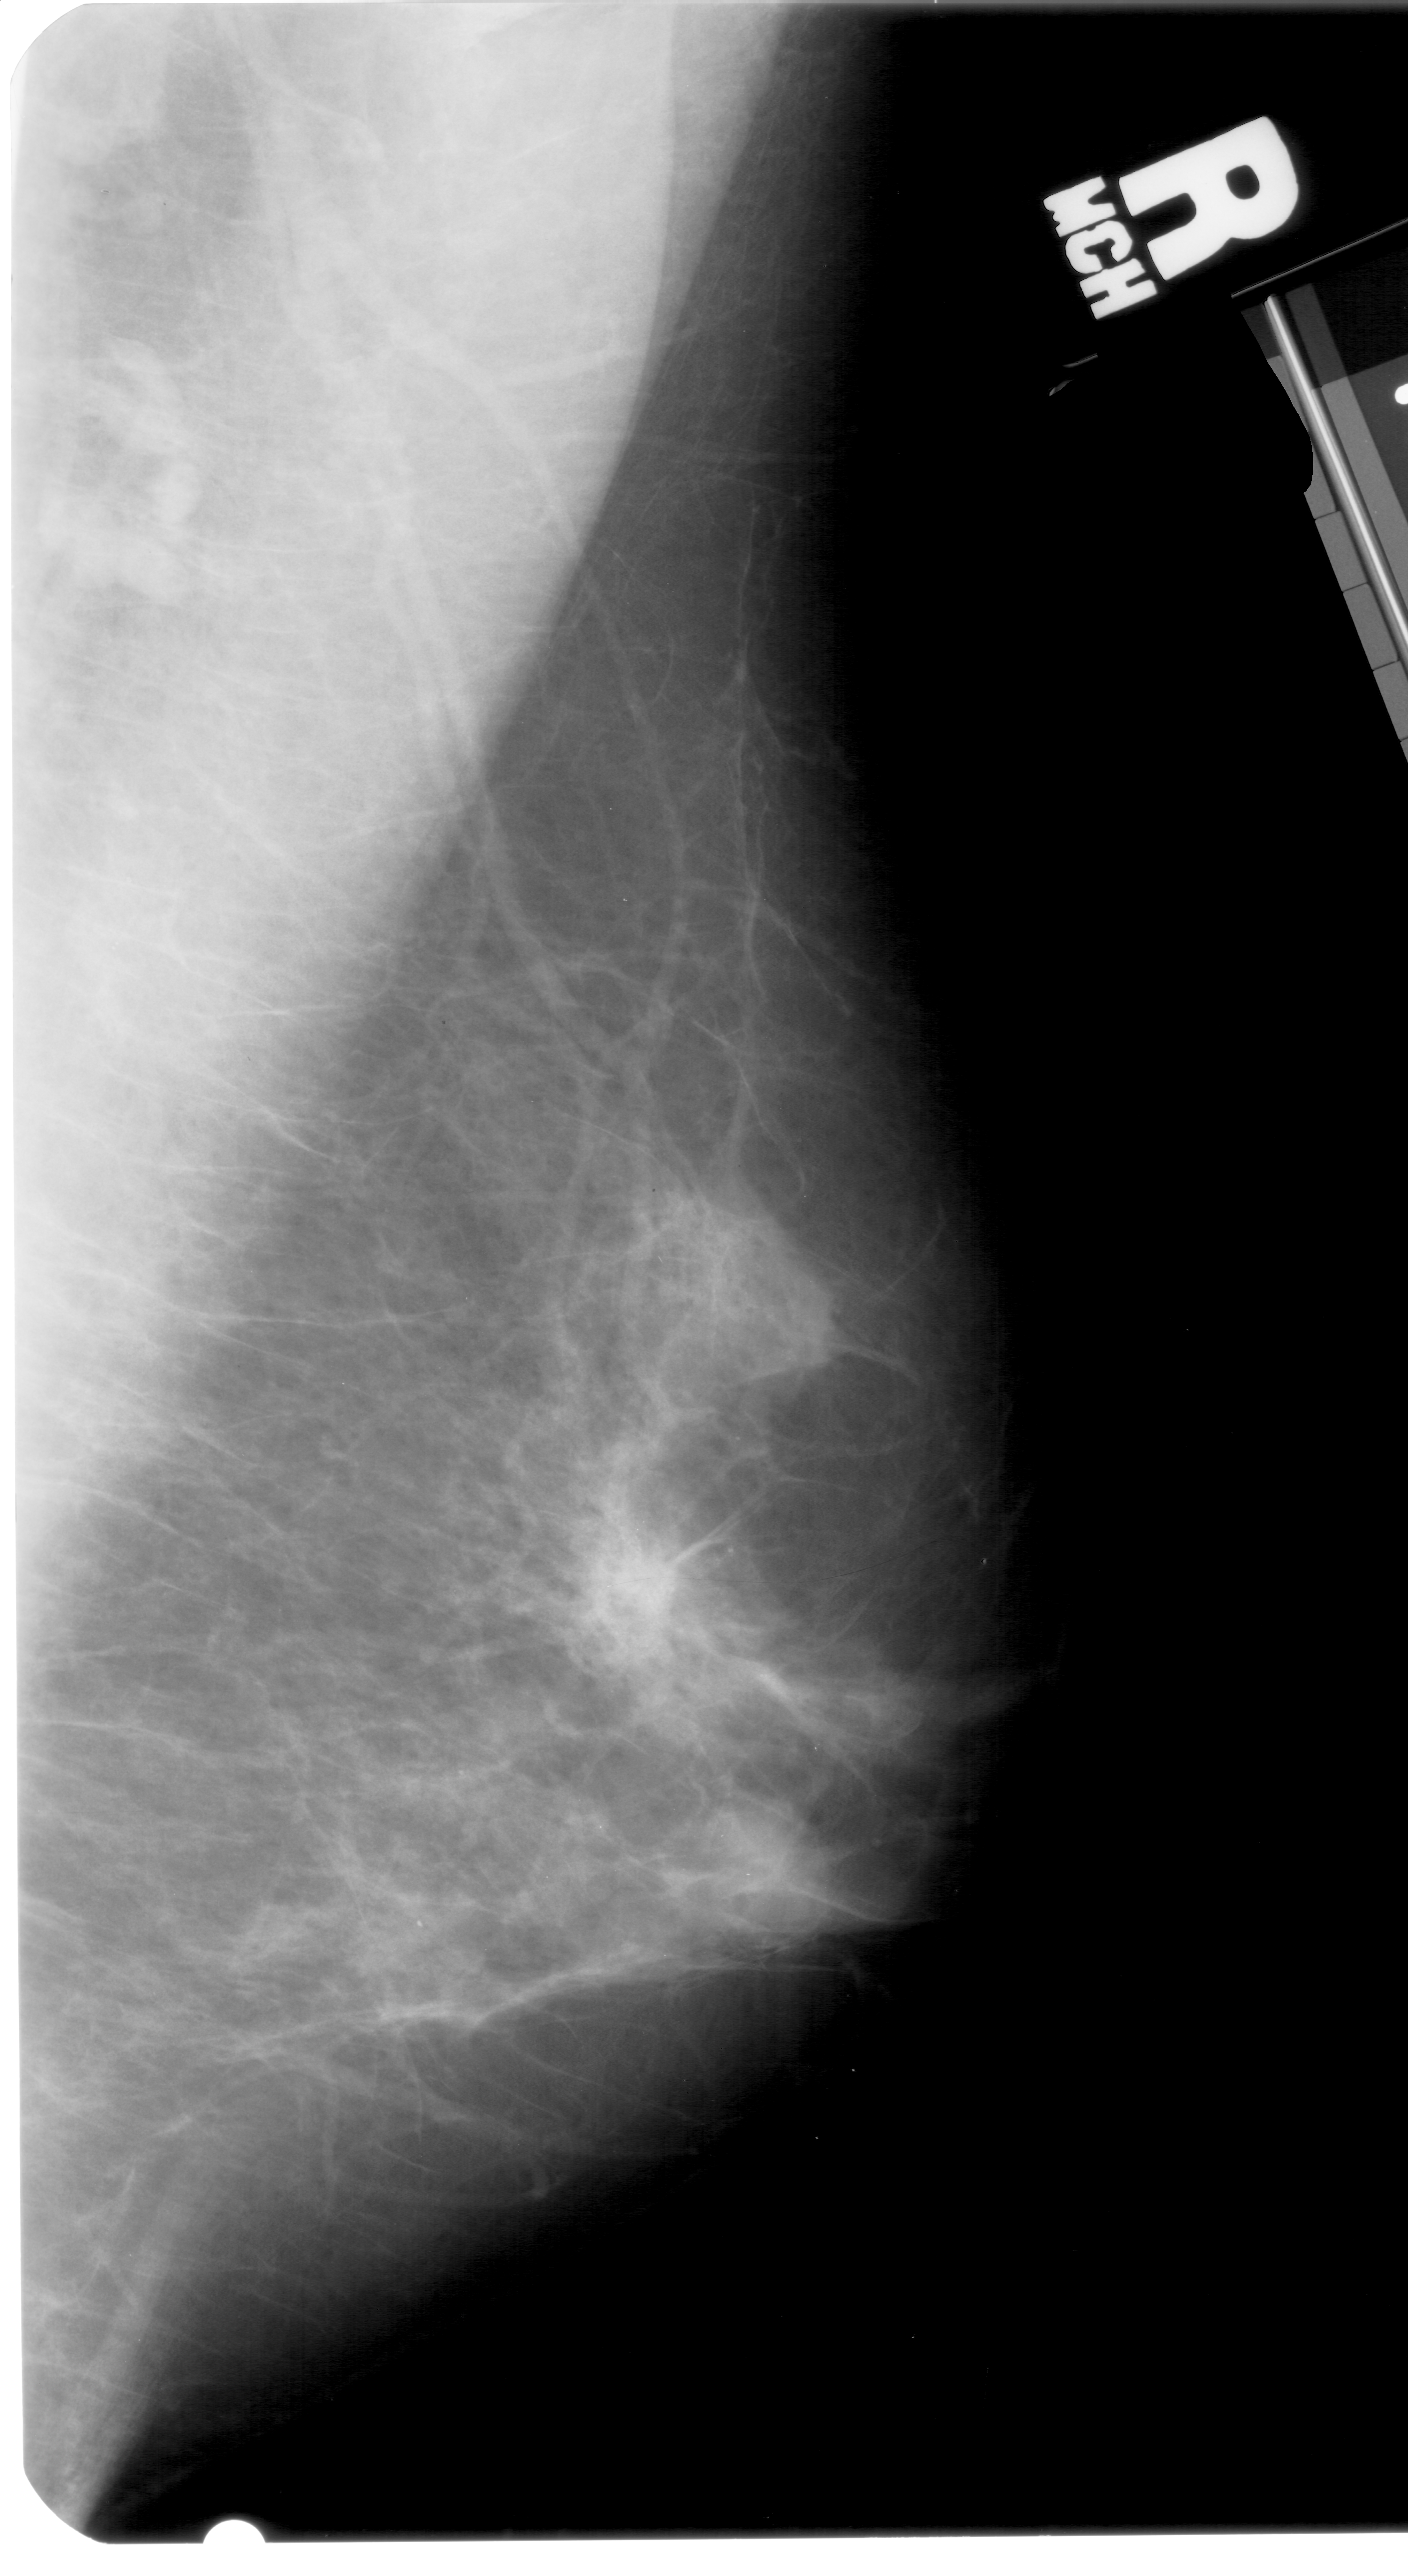
Scanned film-screen mammogram. Right breast. MLO view. BI-RADS breast density category 4 (scale 1–4). 1408 × 2576 image matrix.
Expert-marked regions of interest on this film, with their recorded descriptors:
- calcifications, morphology pleomorphic, distribution clustered; BI-RADS assessment category 4; pathology (as recorded): malignant: bounding box (x1, y1, x2, y2) in pixels: (561, 1467, 732, 1684)